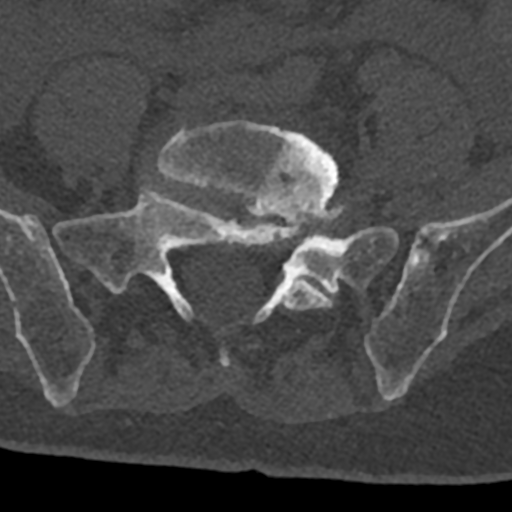
CT including the spine, one axial slice. Position 171 of 797 along the scan axis. Reconstruction kernel Br40s/3. Bone window (W 1800 / L 400 HU). 512 × 512 image matrix, field of view 160 × 160 mm. Patient: male, 74 years. From the clinical record (not read from this slice): primary cancer: renal; vertebrae with lytic lesions (as recorded): T10, L1, L2, L3, L4, L5.
Annotated regions visible in this slice (semi-automatically segmented with operator editing):
- L5 vertebra: box from (x=157, y=121) to (x=339, y=367) px